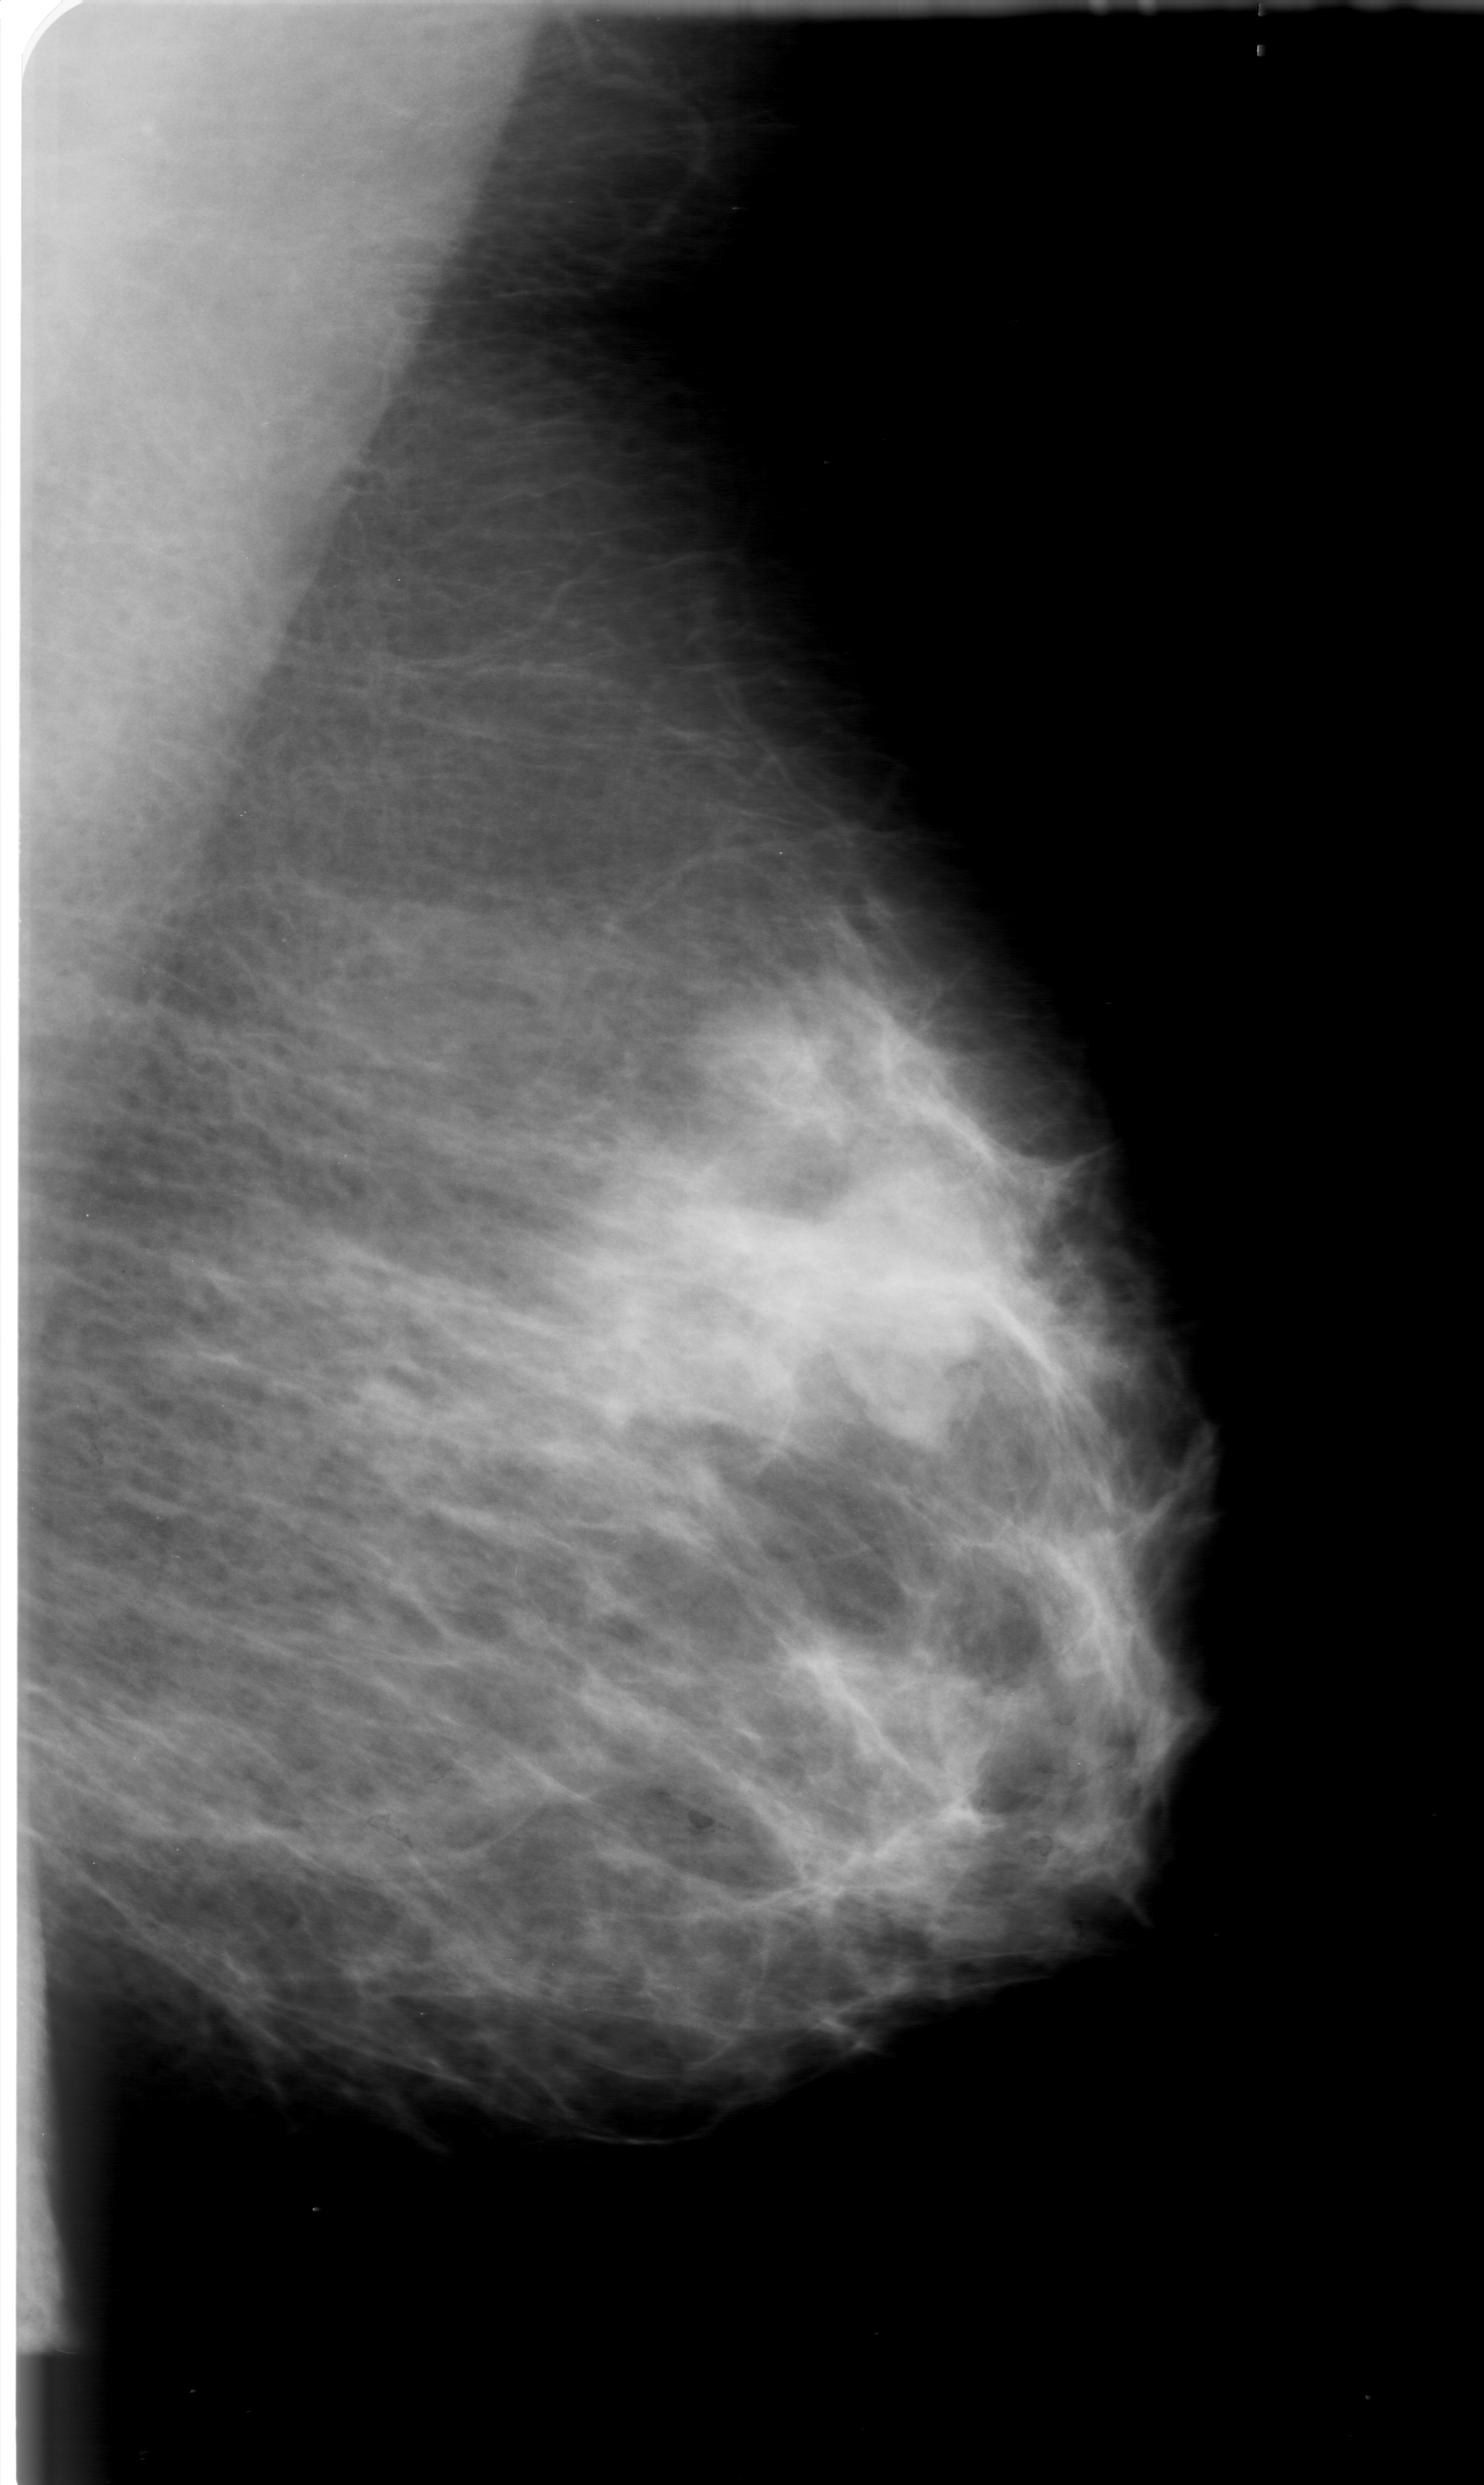
Mammogram (digitized film), left breast, MLO view, BI-RADS breast density category 3 (scale 1–4).
- Mass, shape lobulated, margins circumscribed; BI-RADS assessment category 0; subtlety rating 5 on a 1 (subtle) to 5 (obvious) scale; pathology result (as recorded, not read from the image): benign.